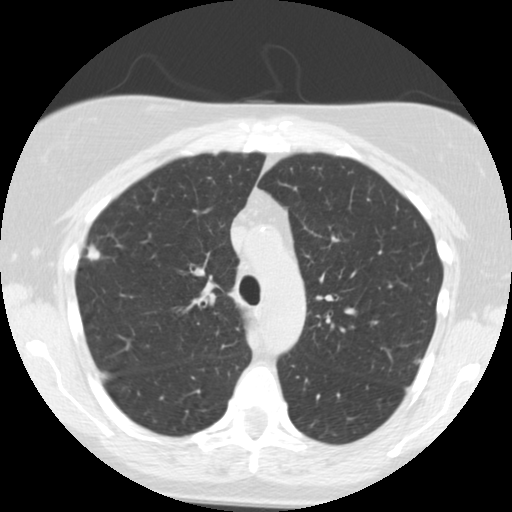
Axial slice from a low-dose chest CT screening exam, second screening round (one year after baseline), lung window (W 1500 / L -600 HU), 2.5 mm slice thickness, standard (soft-tissue) reconstruction kernel (STANDARD), slice 169 of 244 in the series, 512 × 512 image matrix. Female, age 55 years at enrolment. Current smoker at enrolment.
- Lesion marked by an expert reader, bounding box (x1, y1, x2, y2) in pixels: (69, 237, 115, 276).
- Screening reader's record for this exam: no non-calcified nodule ≥4 mm recorded.
- Later outcome: lung cancer diagnosed 621 days after this screen (after the third annual screen) — bronchiolo-alveolar adenocarcinoma, NOS, right upper lobe, moderately differentiated (G2), stage IIA (AJCC 6th edition), 13 mm at pathology.